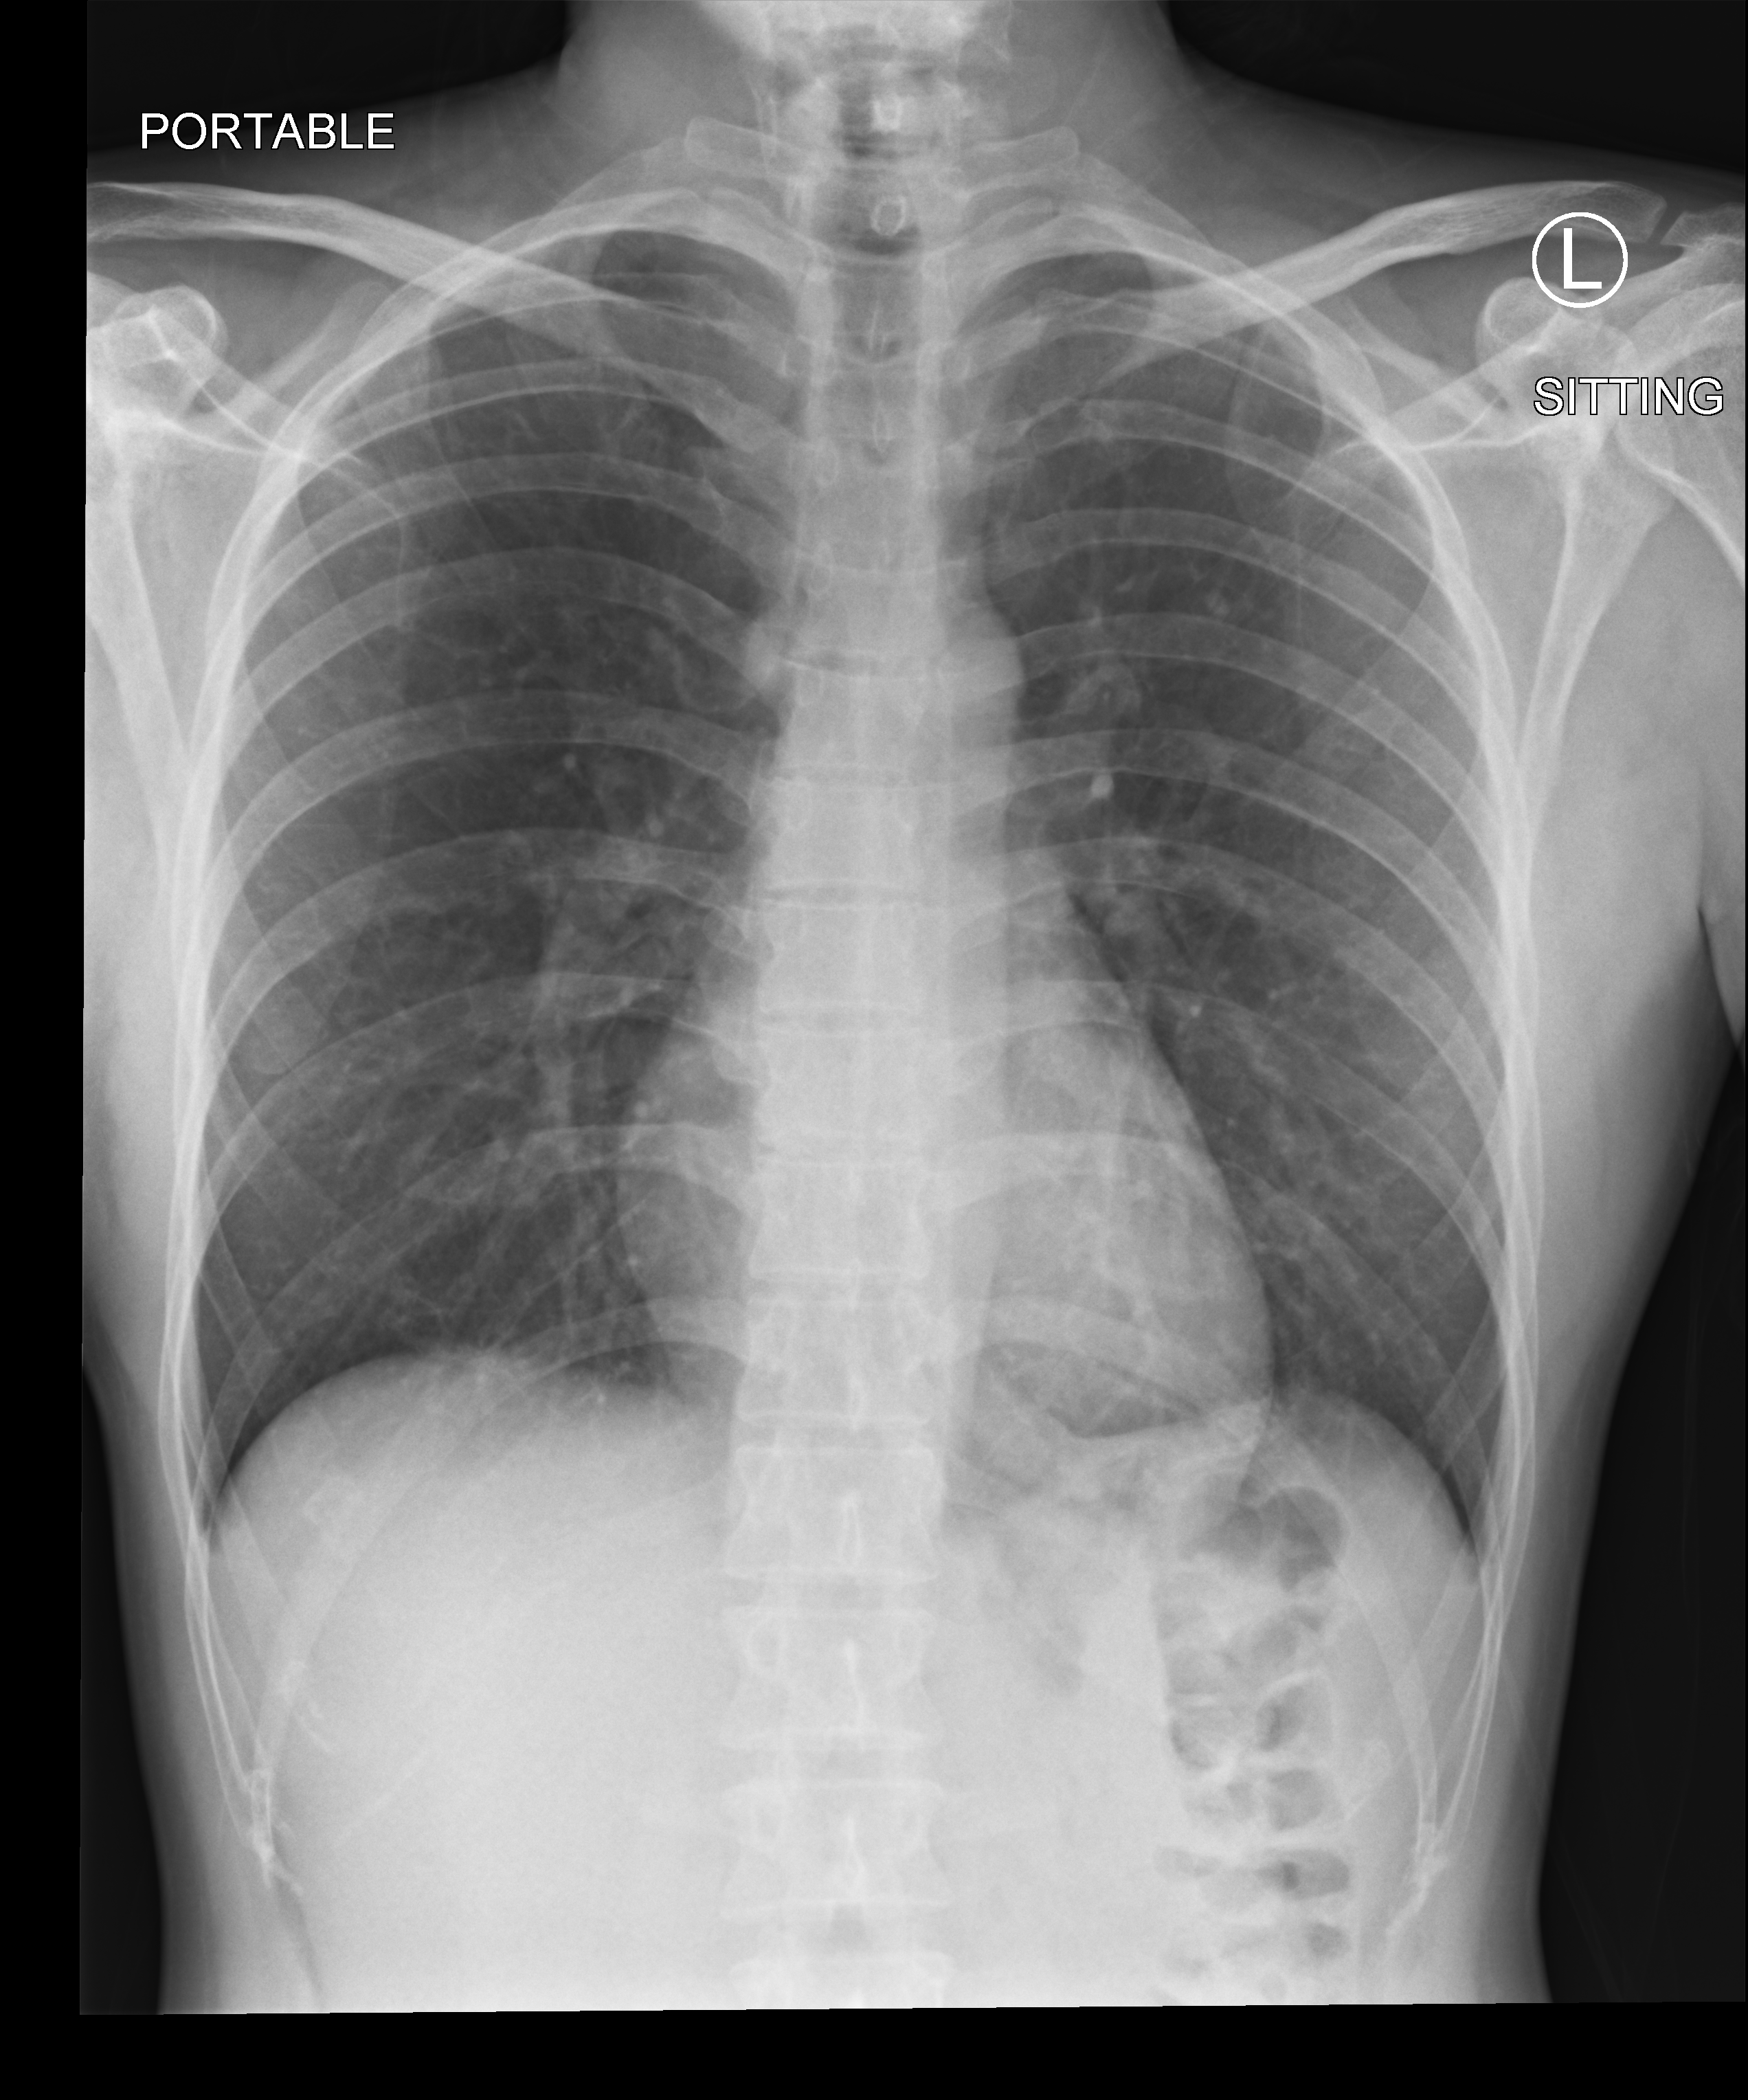
Bedside chest radiograph (computed radiography); anteroposterior (AP) projection. Patient hospitalised with COVID-19; male, aged 18–59 years.
Hospital-stay facts (about this admission, not read from this image; timing relative to this image not recorded):
- chronic kidney disease (admission record): no
- mechanically ventilated during this hospital stay: no